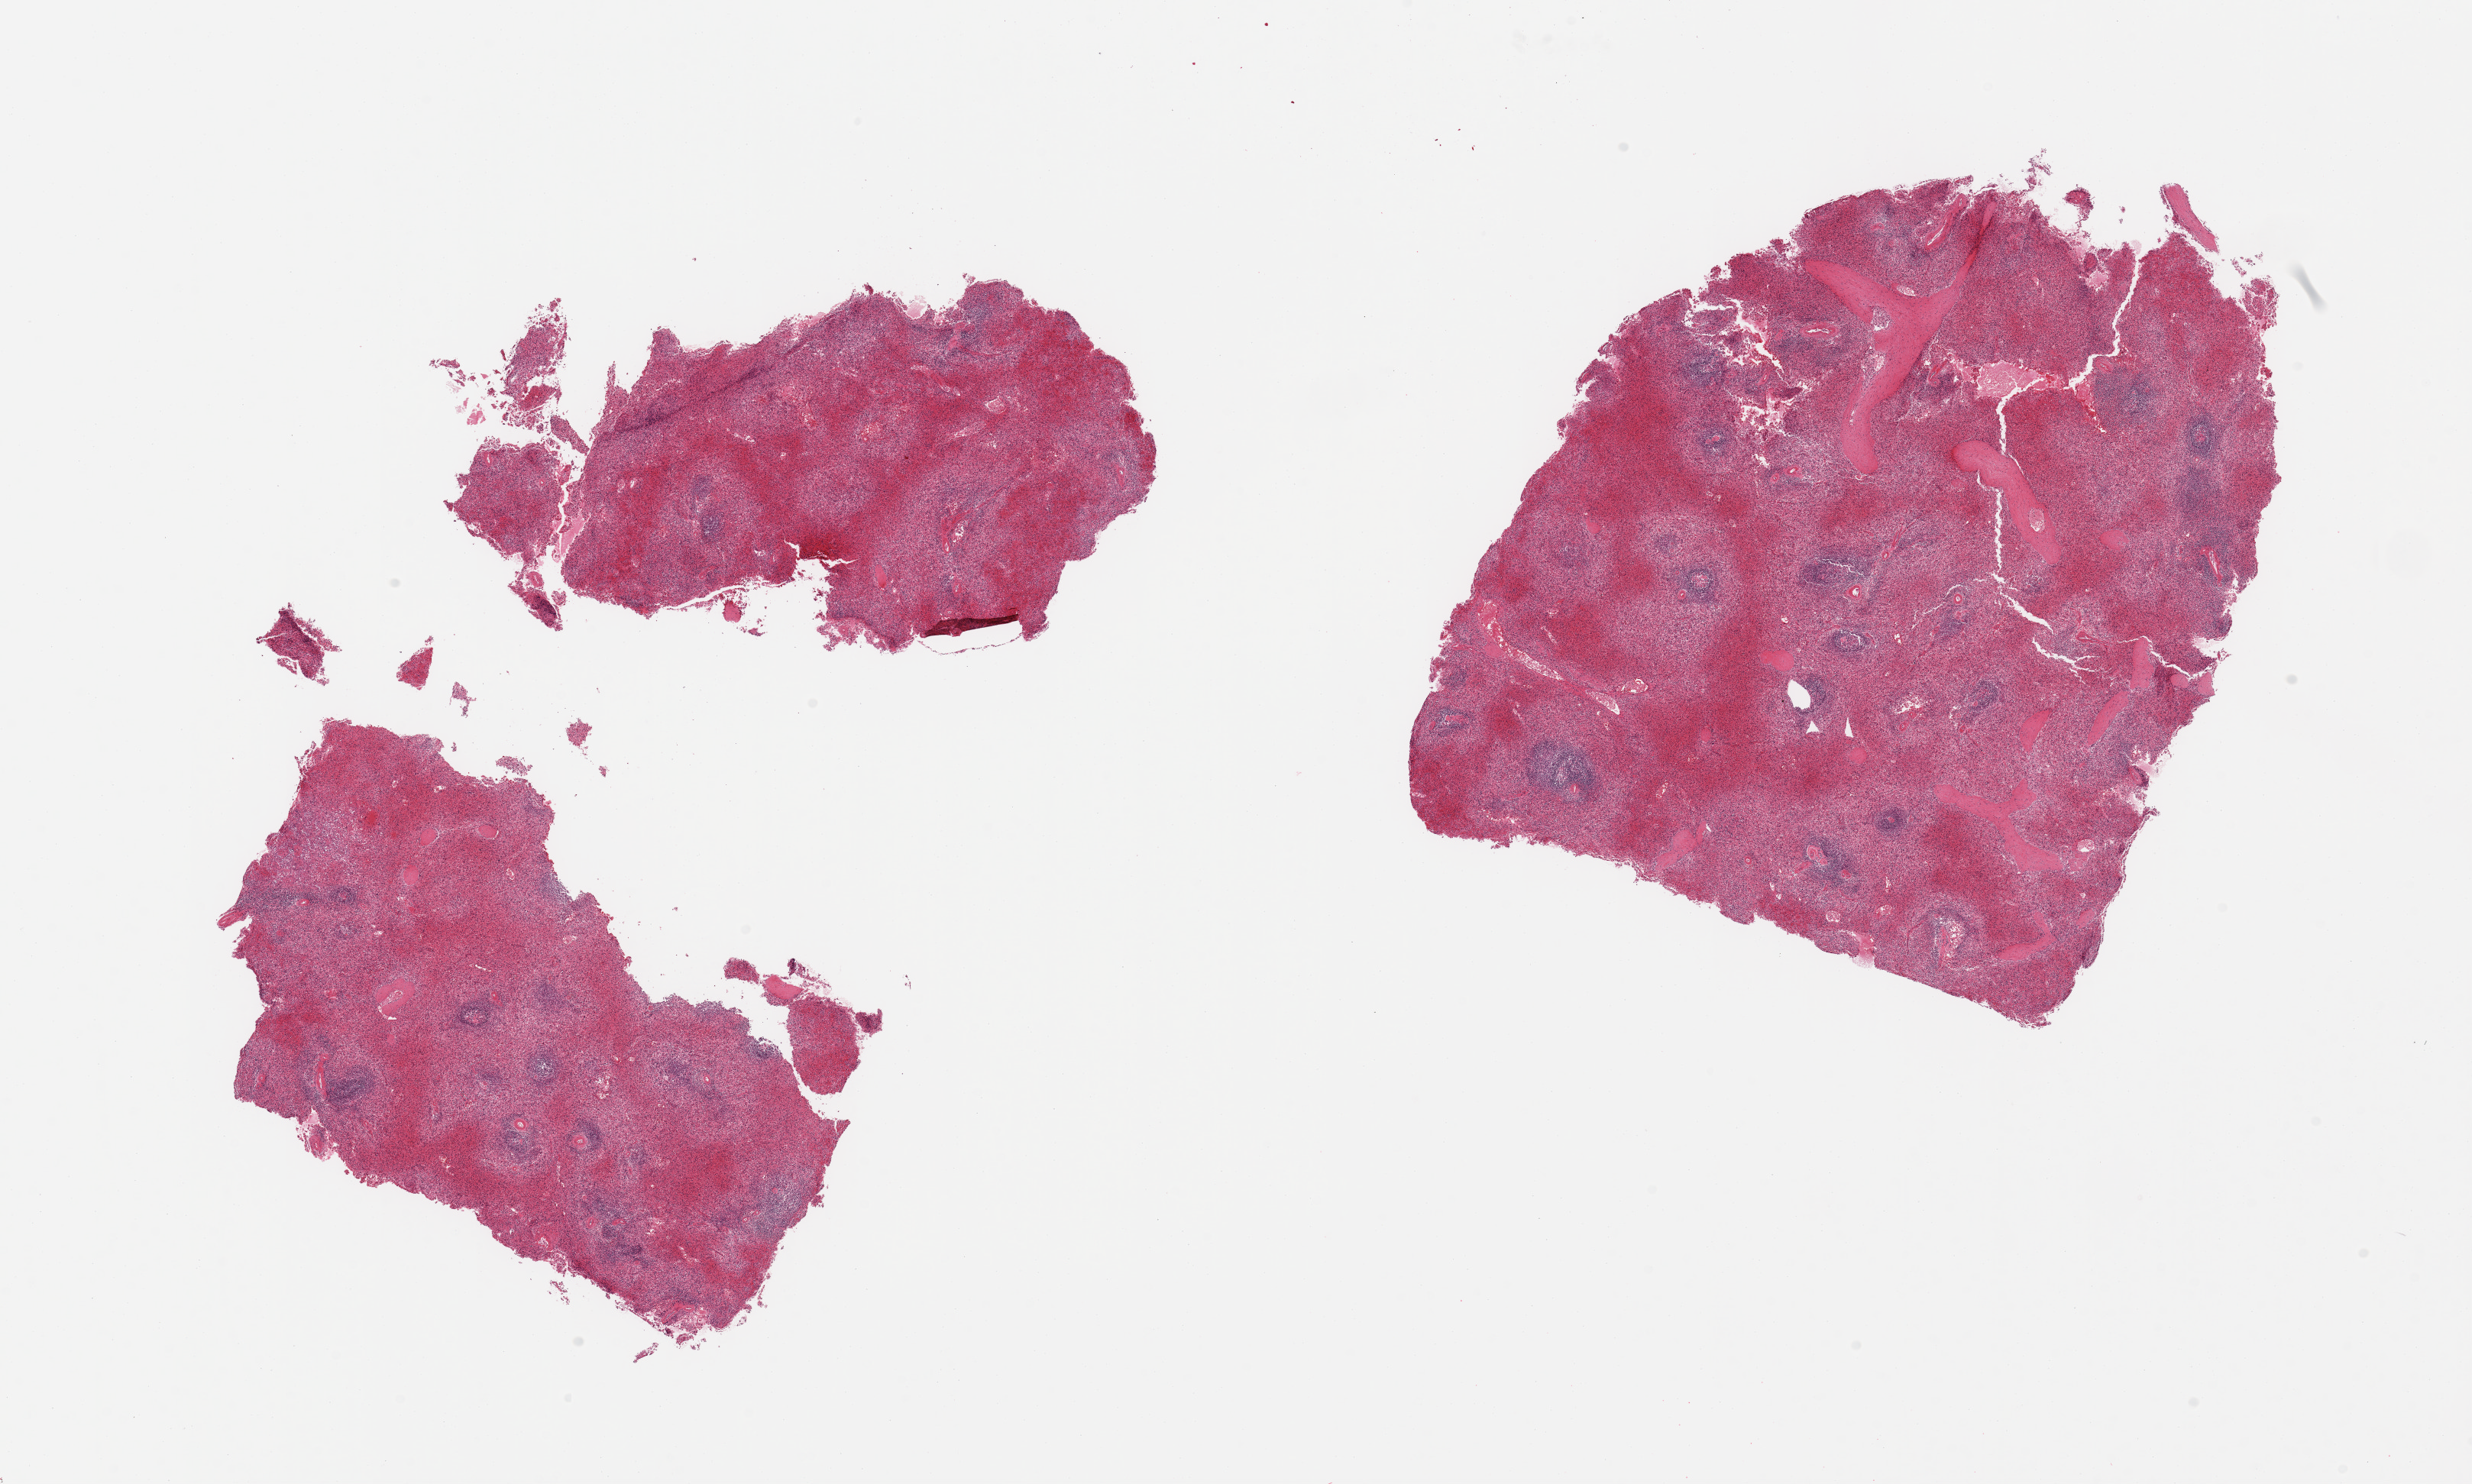
Hematoxylin and eosin (H&E) whole-slide image — a low-resolution overview of the entire scanned area, about 25.6 x 15.4 mm (acquisition: 20x scan), PAXgene-fixed, paraffin-embedded tissue, sampled site (target tissue): spleen, tissue donor sample. Male donor.
Pathologist's review note for this sample: 2 fragmented pieces; moderate red pulp congestion.